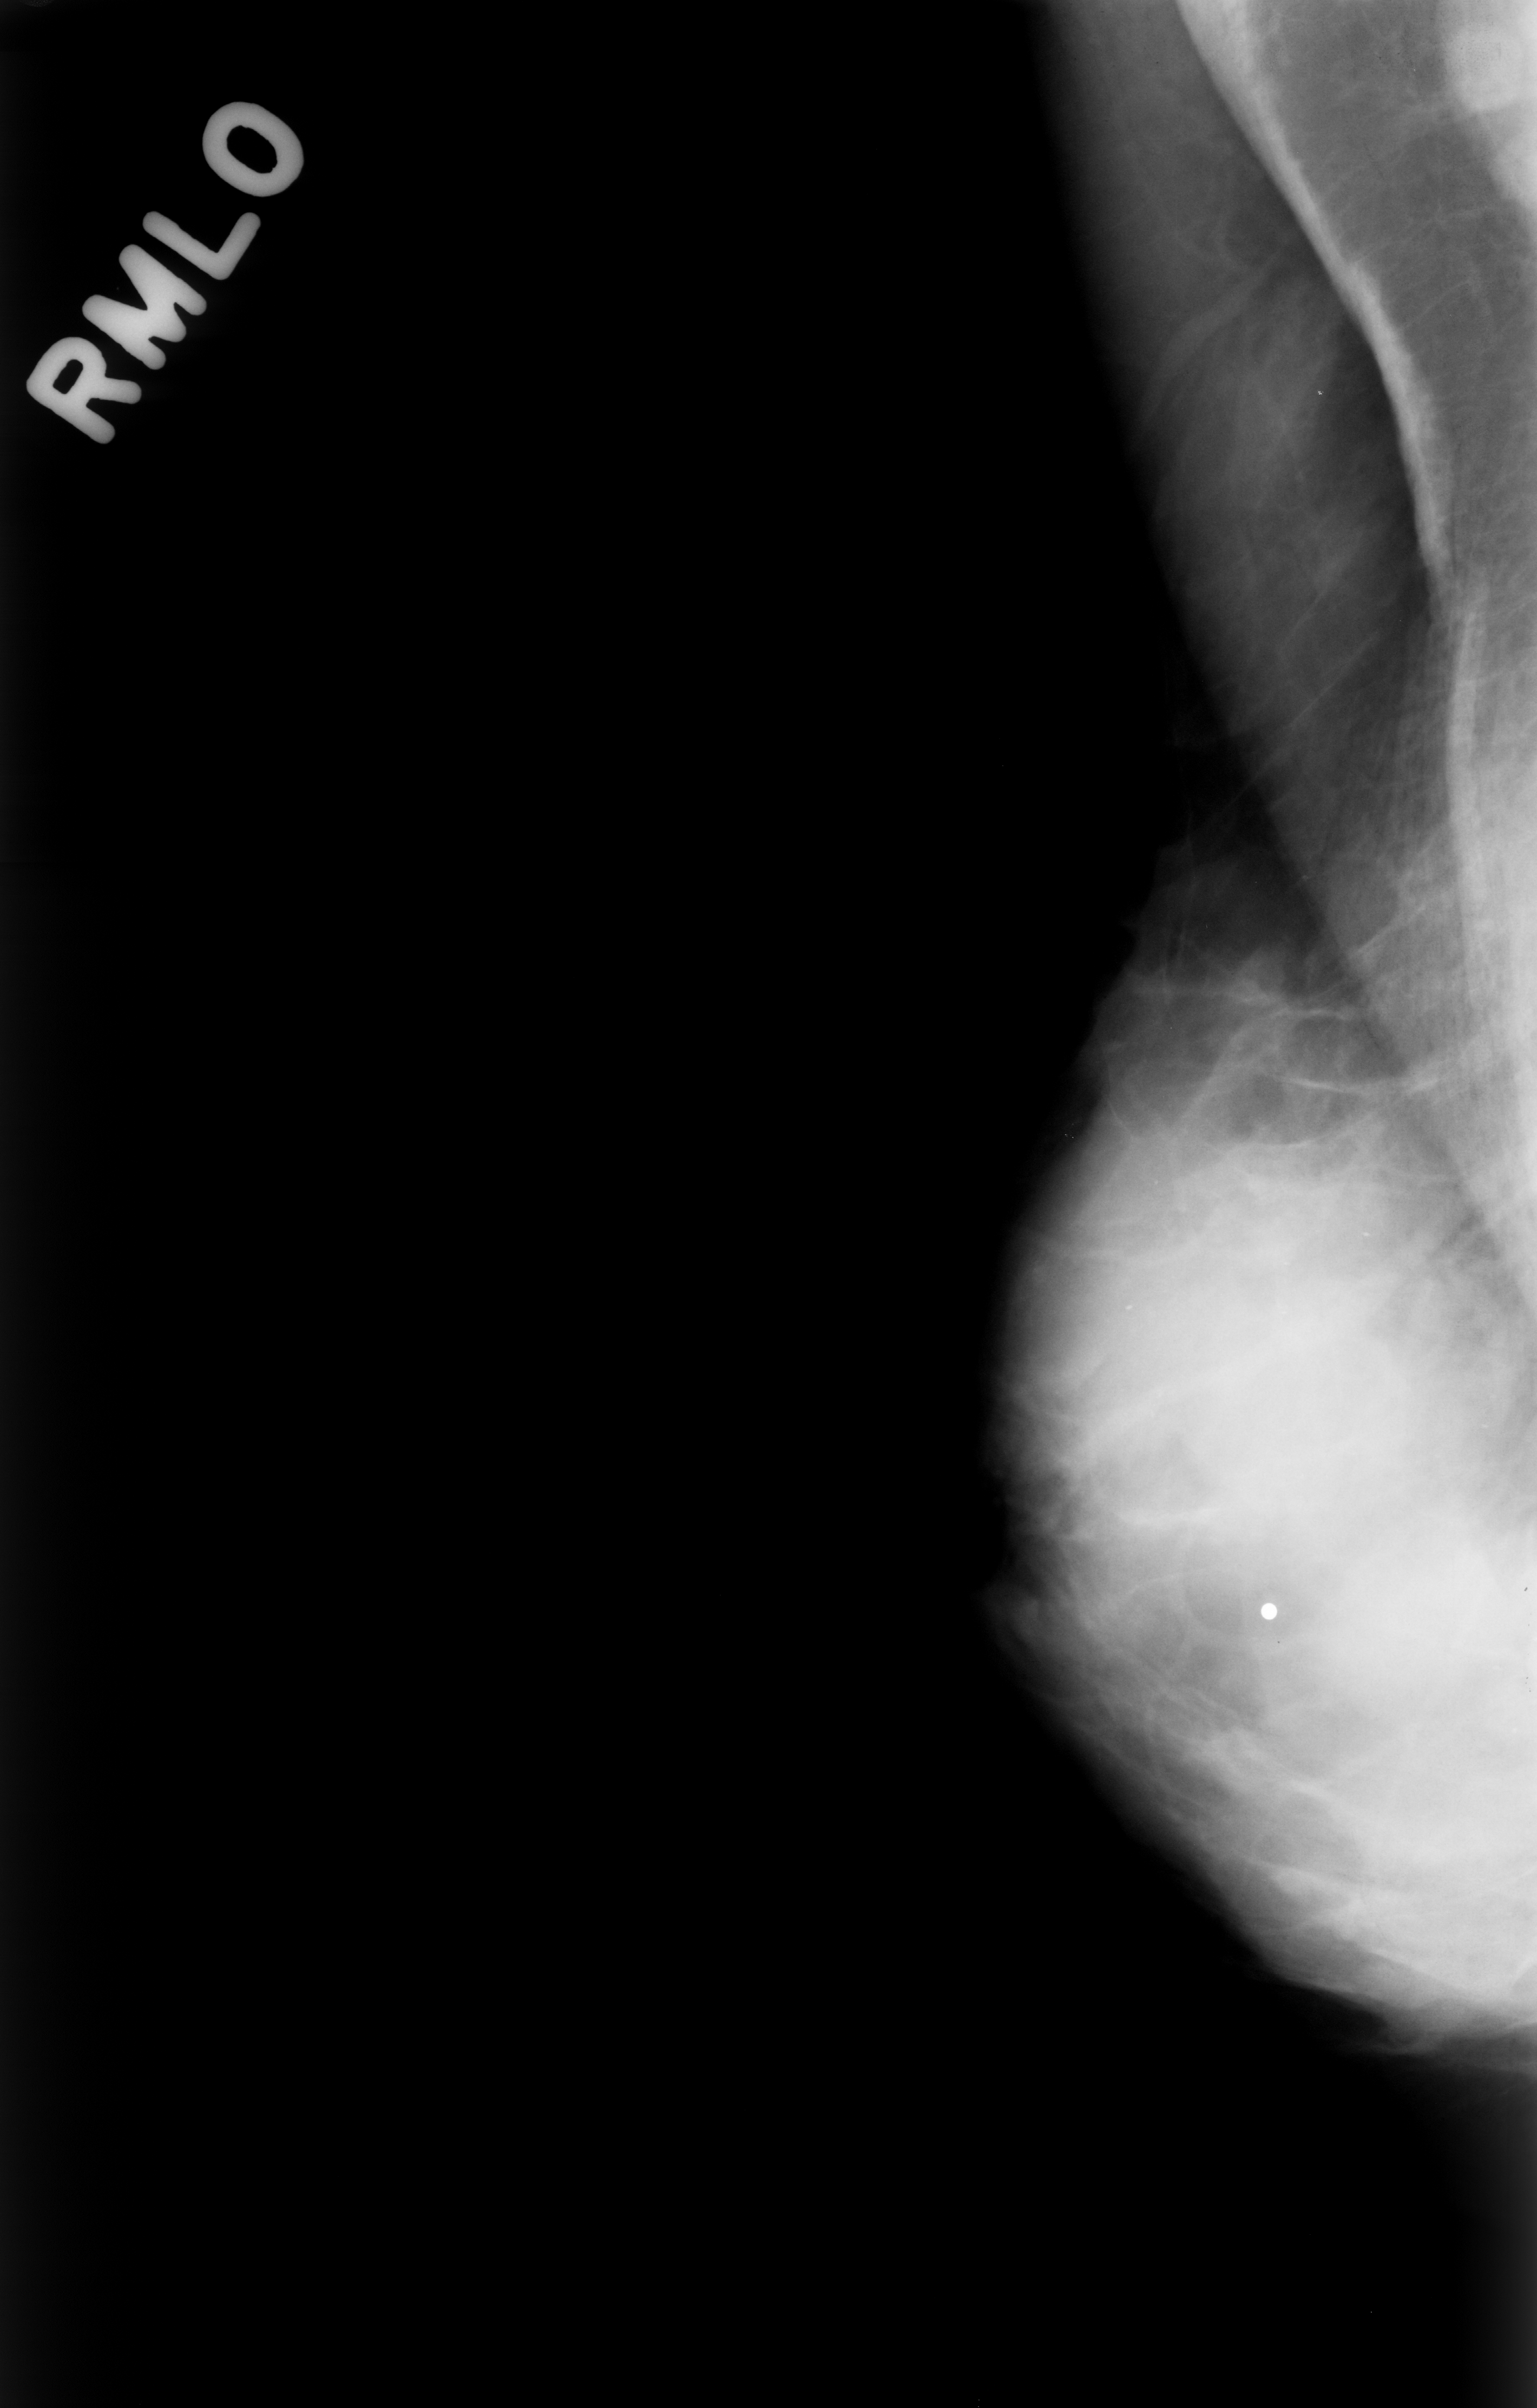
Scanned film-screen mammogram, right breast, mediolateral oblique (MLO) view, BI-RADS breast density category 4 (scale 1–4).
Marked findings (only marked abnormalities are described; nothing is implied about the rest of the image): calcifications, morphology punctate, distribution diffusely scattered; BI-RADS assessment category 2; subtlety rating 4 on a 1 (subtle) to 5 (obvious) scale; pathology (as recorded): benign.